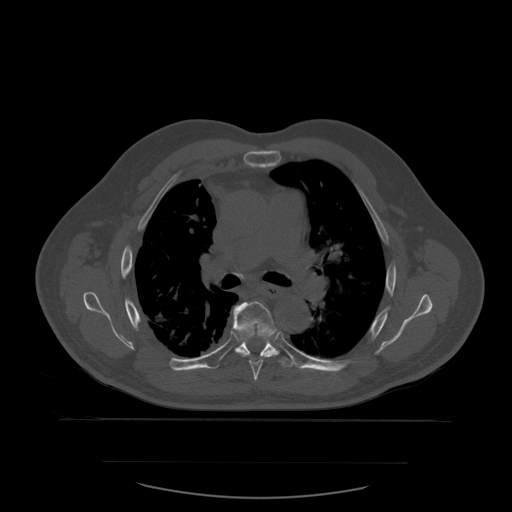
CT including the spine, one axial slice. Slice 396 of 590 in the series (ordered by position). Bone window (W 1800 / L 400 HU). 1.25 mm slice thickness. 512 × 512 image matrix. Patient age 71 years. From the clinical record (not read from this slice): primary cancer: lung.
Structures marked on this image (semi-automatic segmentation, software-assisted and operator-edited):
- T6 vertebra: box from (x=233, y=302) to (x=277, y=381) px
- T7 vertebra: (x=232, y=305)–(x=294, y=368)